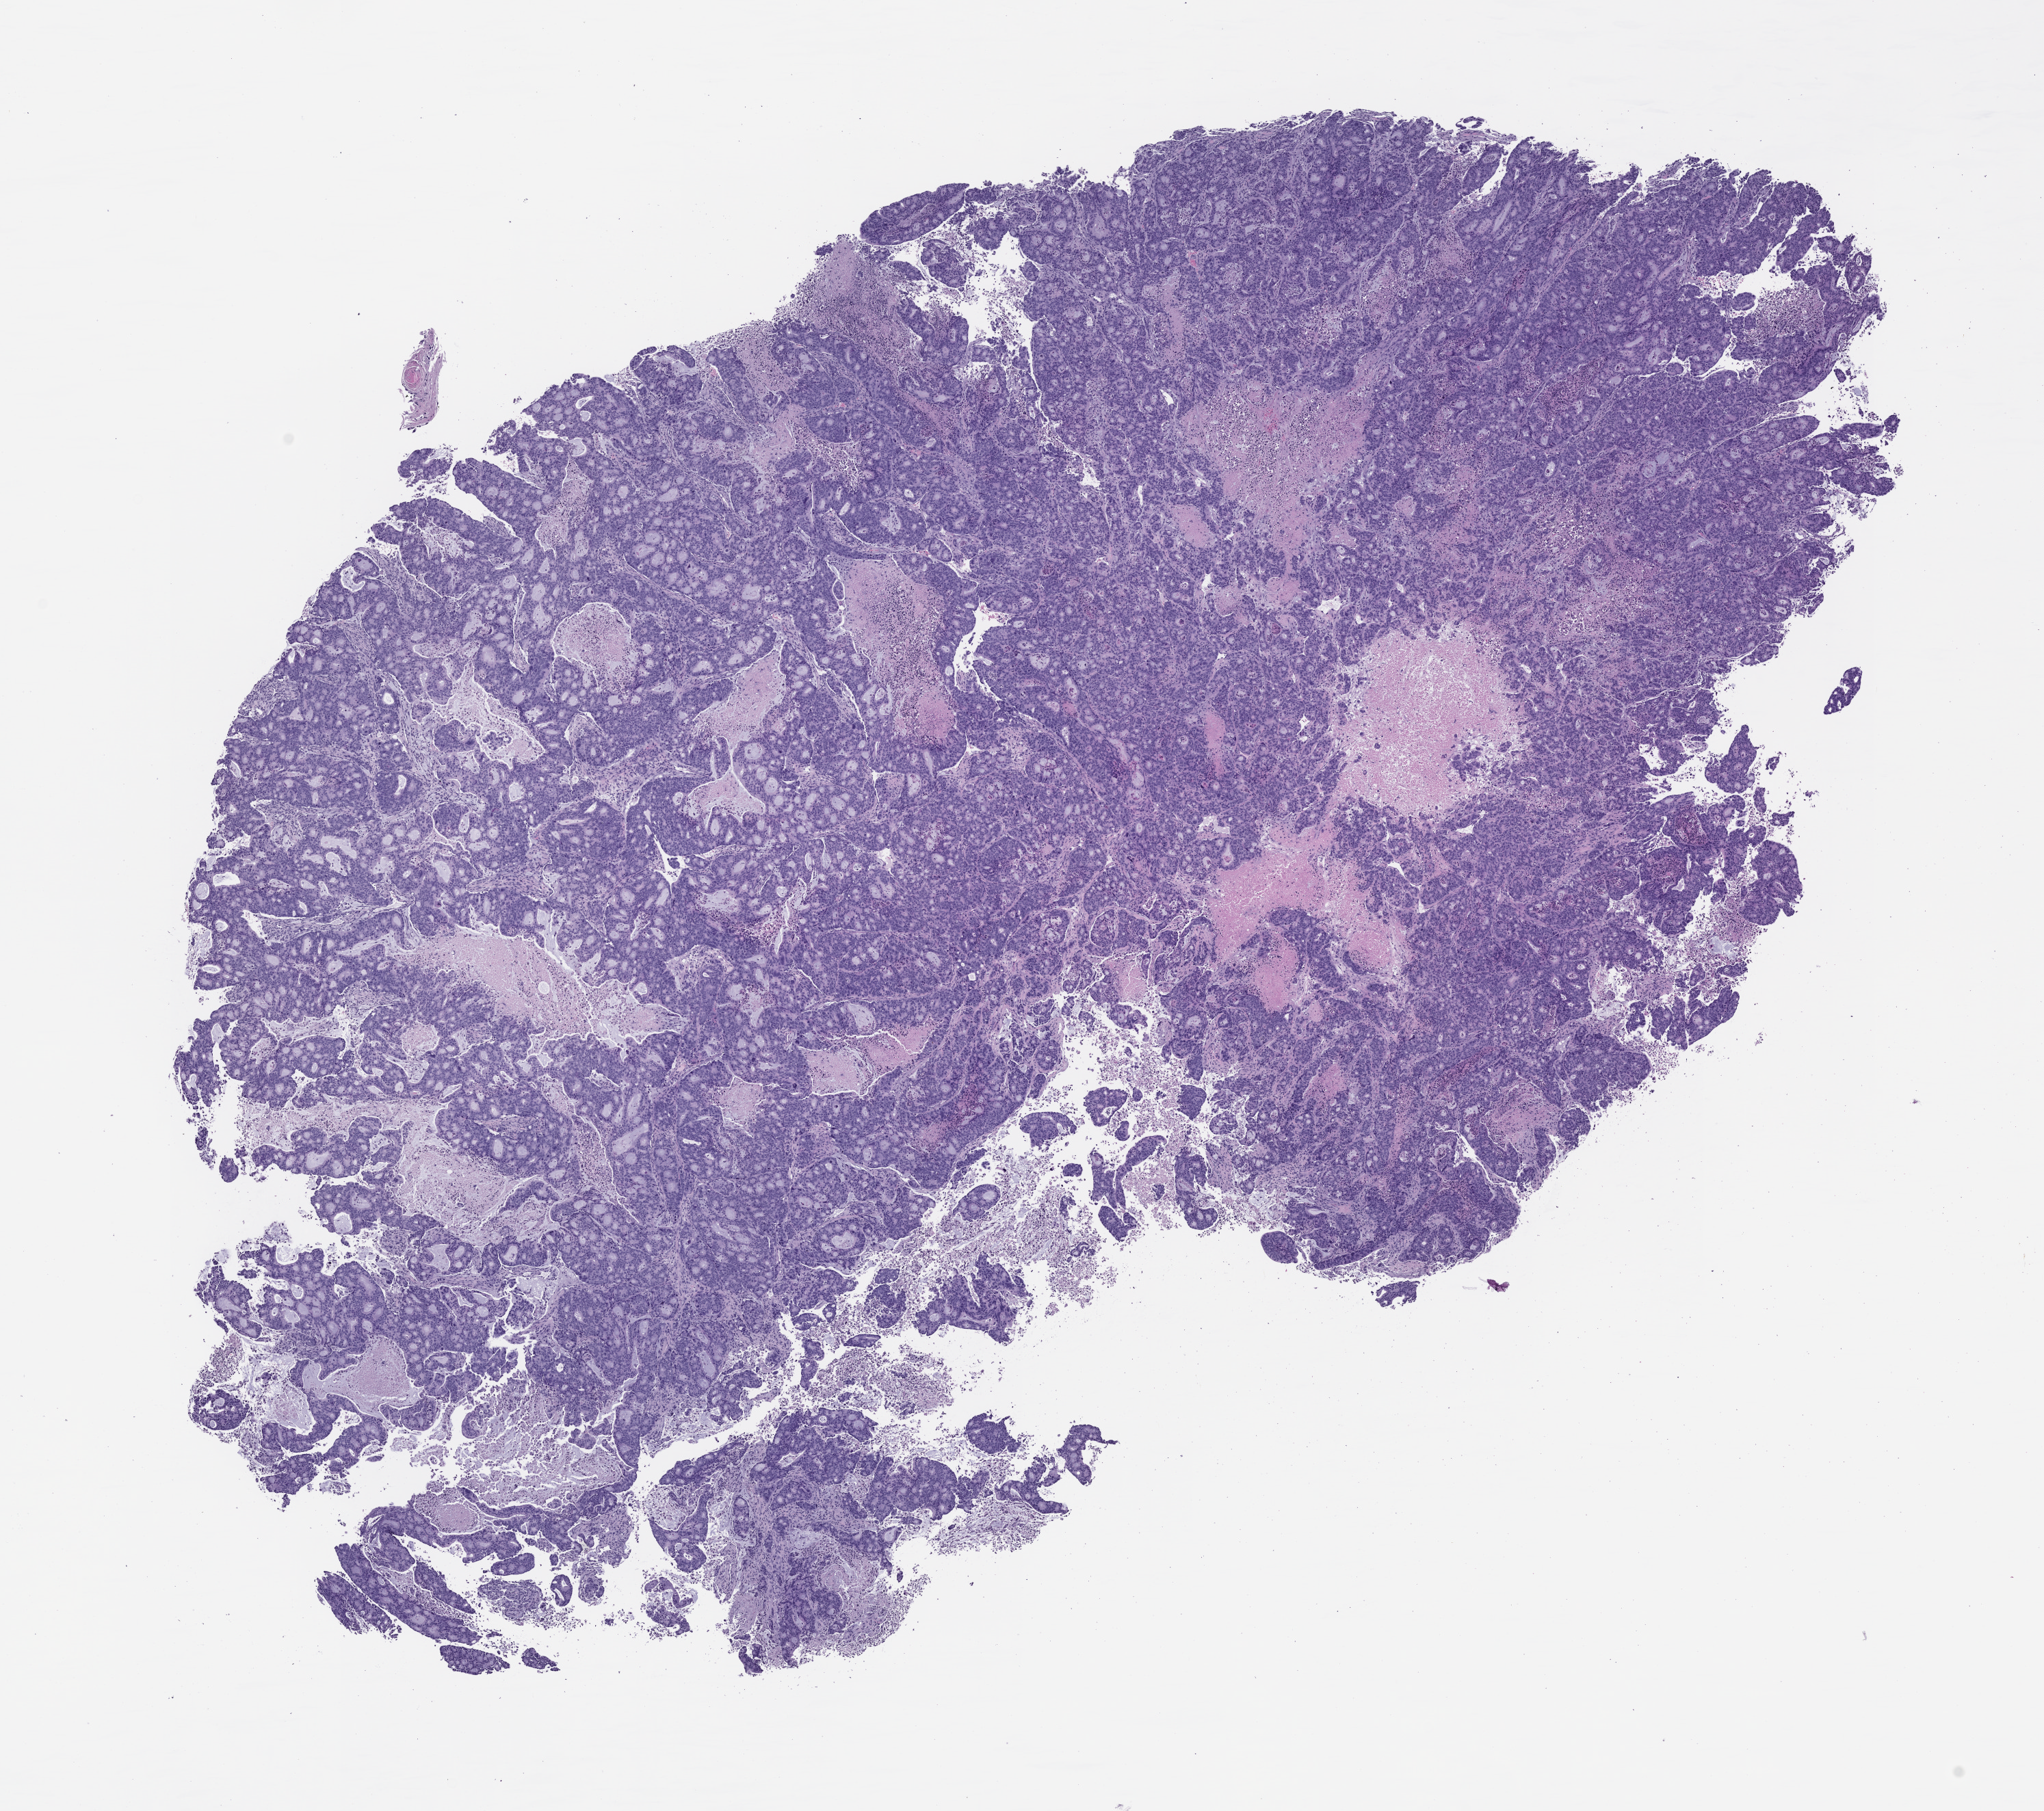
Whole-slide image, haematoxylin and eosin: patient-derived xenograft (human tumor grown in a mouse), passage 0, low-resolution overview of the scanned area, about 12.0 x 10.6 mm. Formalin-fixed paraffin-embedded section. Originating tumor site category: colon.
Originating patient diagnosis: Colon Adenocarcinoma.